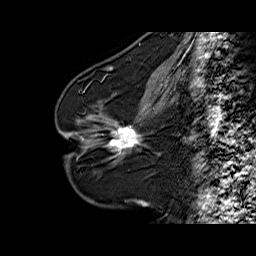
Breast MRI (dynamic contrast-enhanced), one sagittal slice; slice 29 of 60 in the series (ordered by position); dynamic contrast-enhanced series, time point 2 of 6 at this slice position (early post-contrast); 1.5 T; TE 6.3 ms, TR 32.5 ms; 4 mm slice thickness; 256 × 256 image matrix, field of view 200 × 200 mm. Female patient. Case-level facts recorded for this patient, not image findings: setting: breast cancer imaged before/during neoadjuvant chemotherapy; receptor status: HR-positive, HER2-negative.
Outlined on this slice (semi-automatically segmented with operator editing):
- analysis volume of interest (the breast-tissue region the enhancement analysis was run in; not a lesion): bounding box [x1, y1, x2, y2] px = [94, 103, 161, 164]
- tumour enhancement mask (voxels above the 100 % enhancement threshold inside the analysis volume of interest): [109, 124, 141, 151]